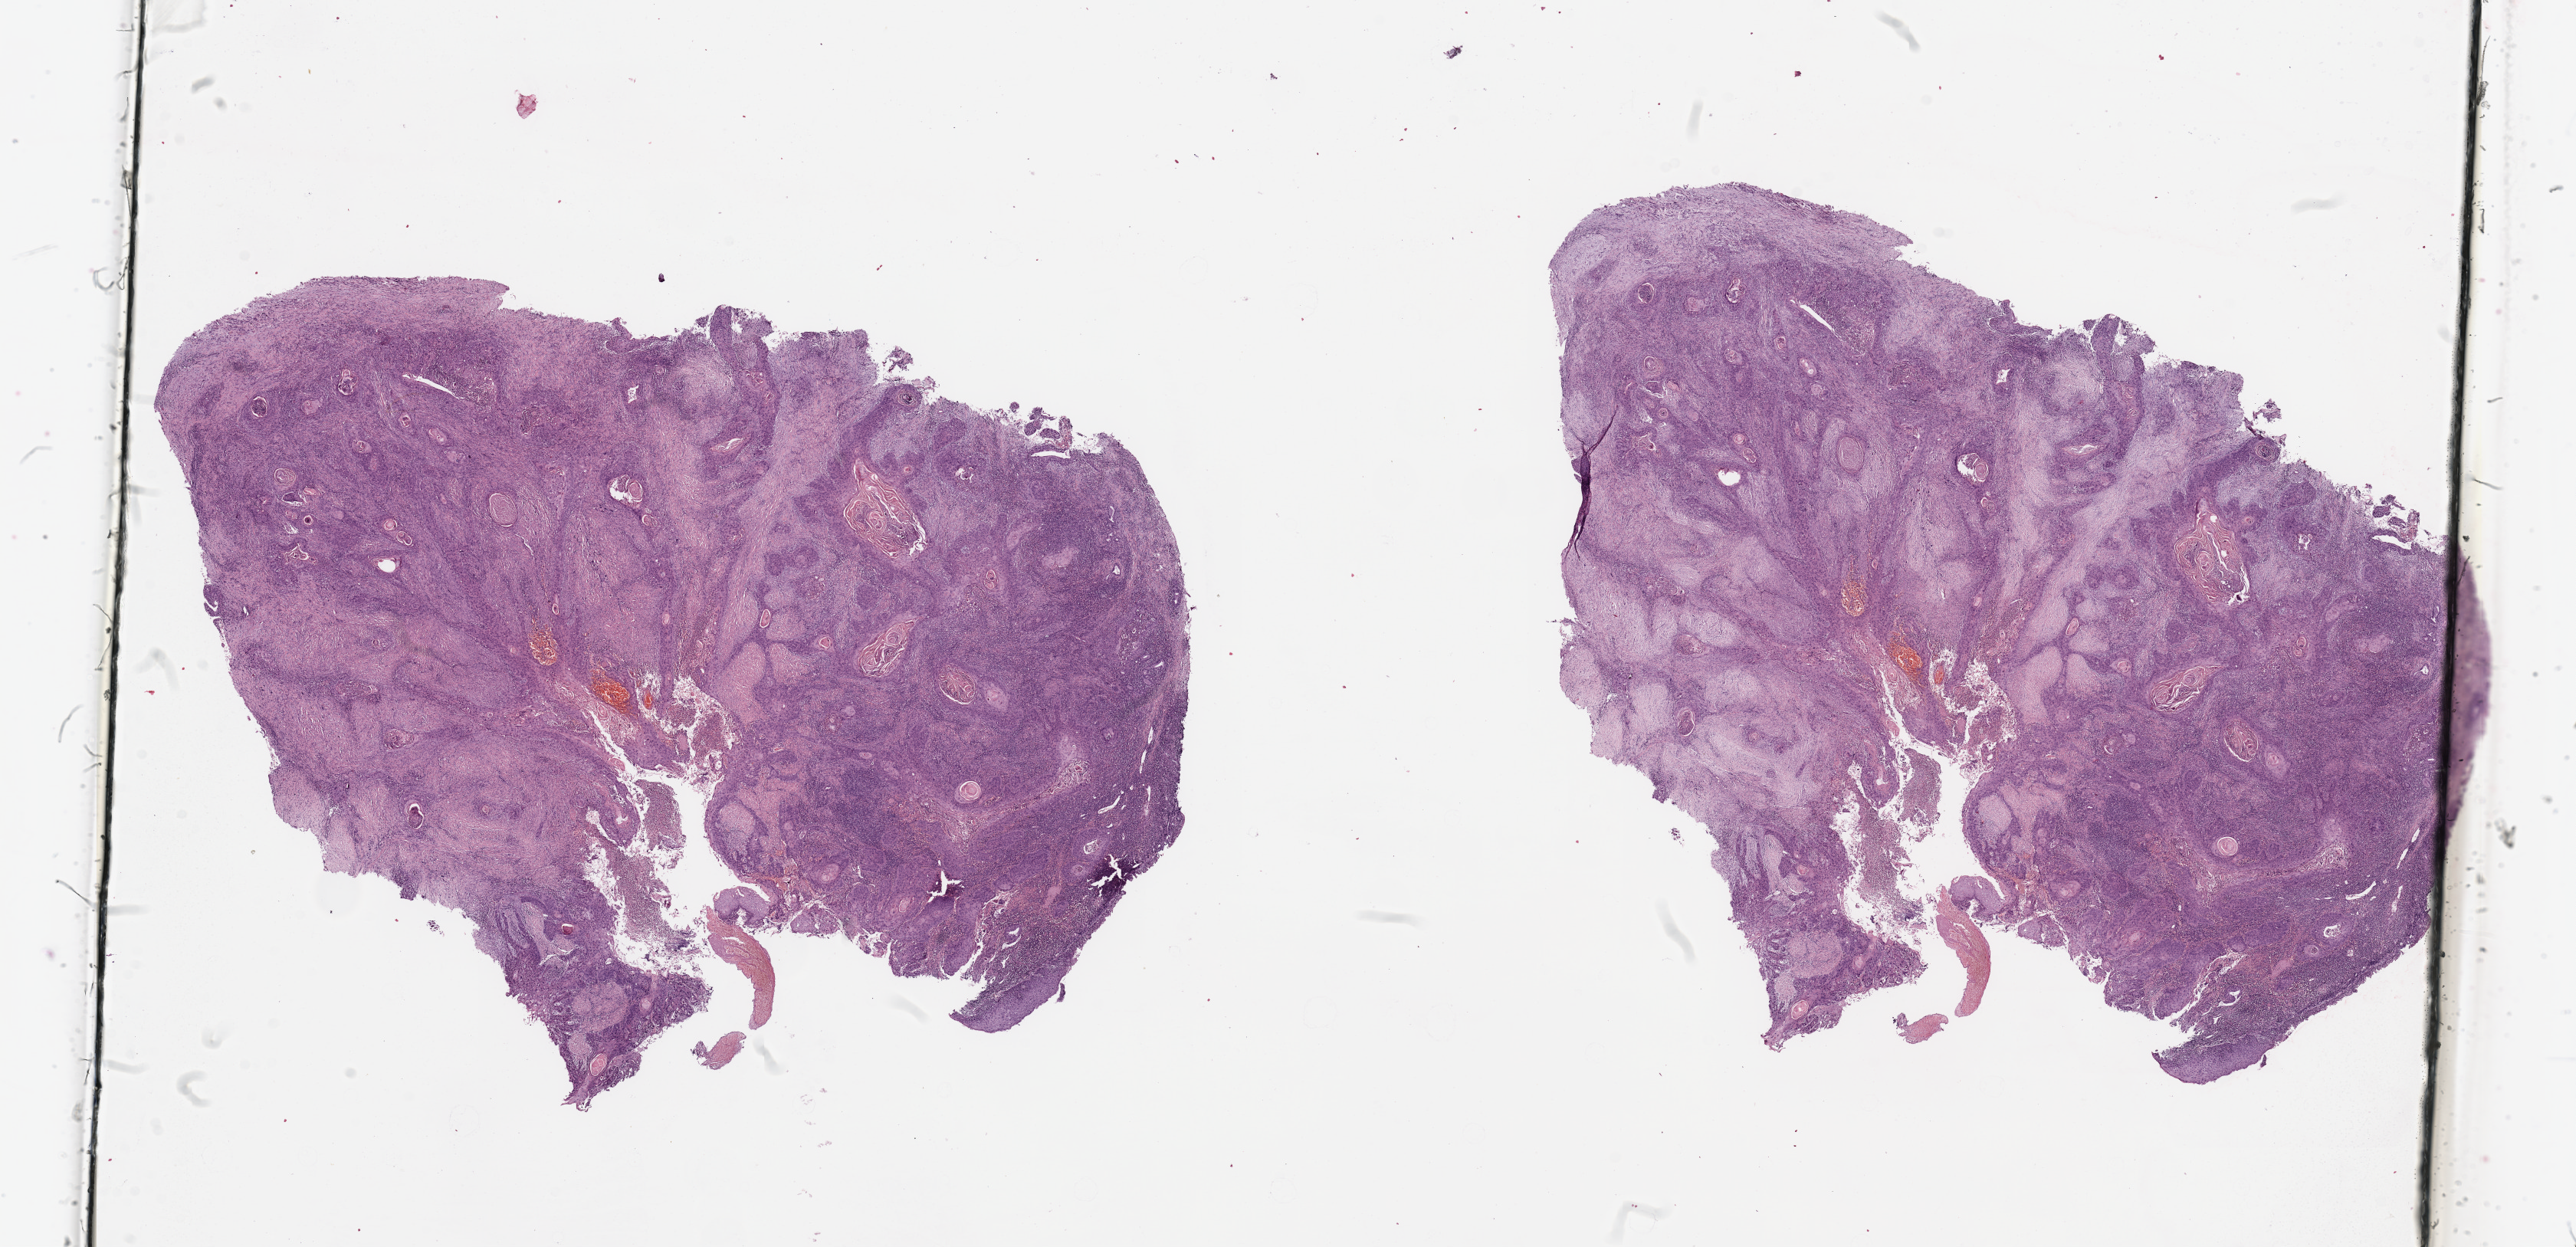
Whole-slide histology image, H&E, shown as a low-resolution overview of the whole scanned area (about 26.6 x 12.9 mm, acquisition: 20x scan). Tumour tissue sample, sampled site: larynx. Male, 49 y/o. Histologic grade: G2 (moderately differentiated). Composition of this section per pathologist review: tumour nuclei 80%, necrosis 2%.
Histologic diagnosis: Squamous cell carcinoma, NOS (larynx, NOS). AJCC pathologic stage: IVA. Primary tumour site (as recorded): larynx.